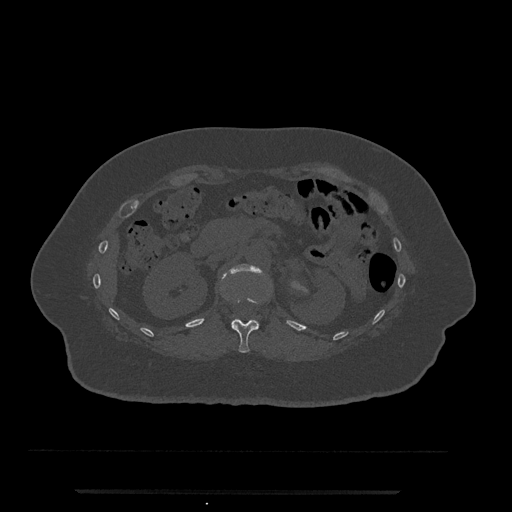
CT including the spine, one axial slice. Slice 145 of 797 in the series (ordered by position). Reconstruction kernel Br40s/3. Bone window (W 1800 / L 400 HU). 0.5 mm slice thickness. 512 × 512 image matrix, field of view 440 × 440 mm. Patient: female, 51 years. Case-level facts recorded for this patient, not image findings: primary cancer: neuro; vertebrae with lytic lesions (as recorded): T8.
Outlined on this slice (semi-automatic segmentation, software-assisted and operator-edited):
- L1 vertebra: bounding box [x1, y1, x2, y2] px = [223, 264, 263, 278]
- T12 vertebra: [231, 298, 261, 353]